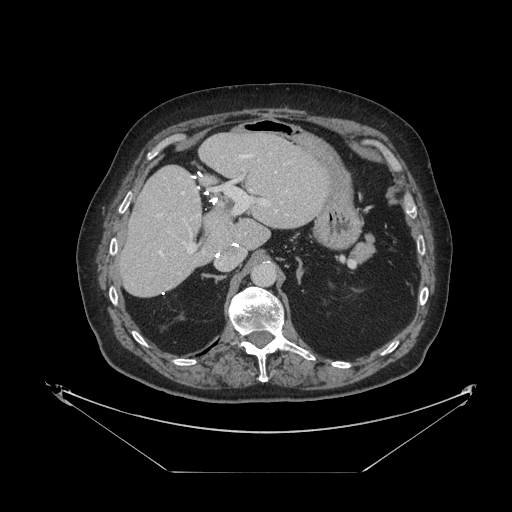
Contrast-enhanced abdominal CT, one axial slice; position 66 of 121 along the scan axis; reconstruction kernel STANDARD; intravenous contrast given; soft-tissue window (W 400 / L 40 HU); 2.5 mm slice thickness; 512 × 512 image matrix, field of view 500 × 500 mm. Male patient, age 68 years. From the clinical record (not read from this slice): diagnosis: colorectal cancer liver metastases, imaged before liver resection; multiple liver metastases: no; largest metastasis: 4 cm; disease in both lobes: no.
Outlined on this slice (outlined manually by an expert reader):
- hepatic veins: bounding box (x1, y1, x2, y2) in pixels: (159, 155, 278, 255)
- liver: (121, 134, 331, 297)
- planned liver remnant (the part of the liver to remain after resection): (121, 134, 331, 297)
- portal vein (with intrahepatic branches): (183, 178, 282, 254)